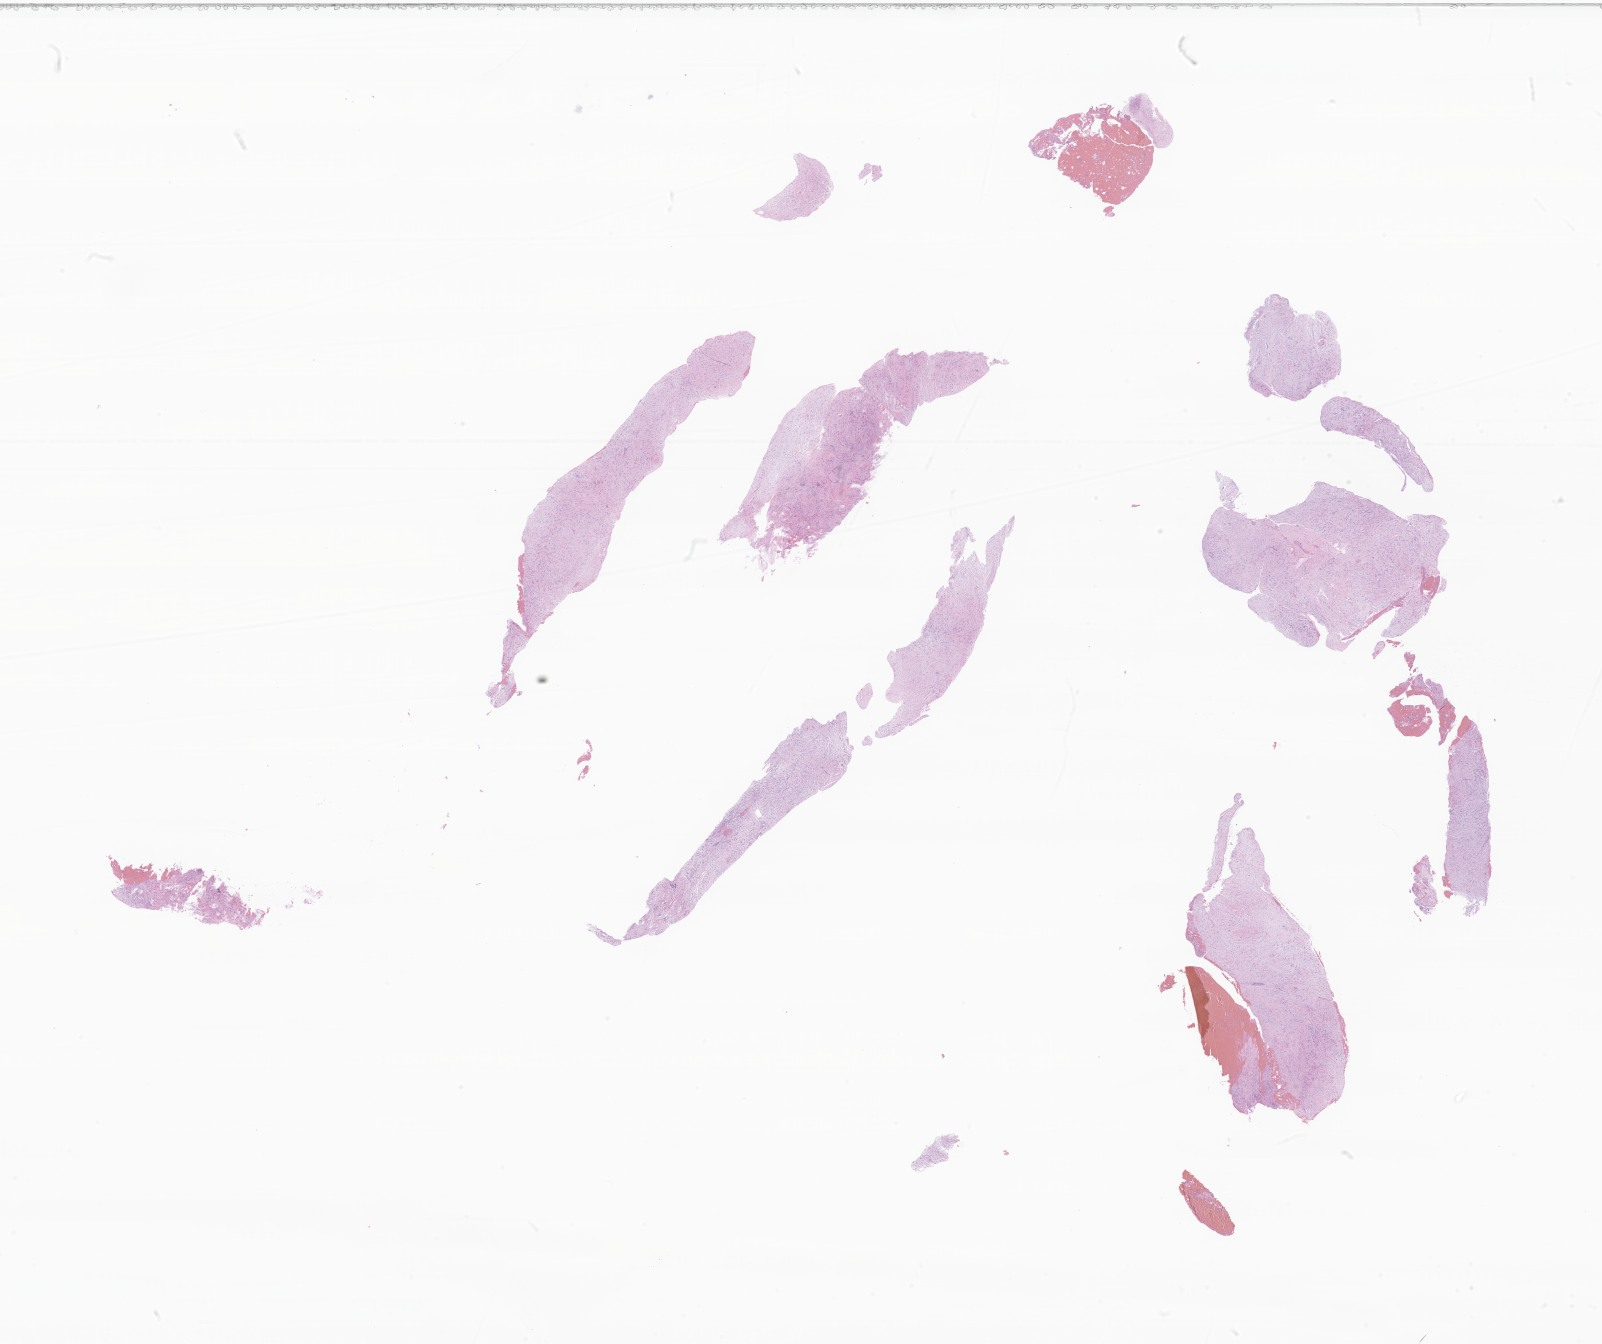
Digitized H&E-stained section of tumor tissue from the pelvis, a low-resolution overview of the entire scanned area, about 27.0 x 22.7 mm, formalin-fixed, paraffin-embedded (FFPE) tissue. Male patient, age 120 months.
• recorded diagnosis: Aggressive fibromatosis